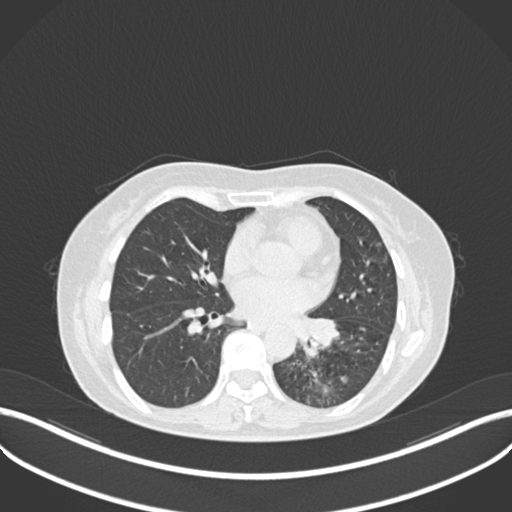
Chest CT, one axial slice; slice 119 of 270 in the series (ordered by position); 120 kVp; lung window (W 1500 / L -600 HU); 1 mm slice thickness; 512 × 512 image matrix, field of view 400 × 400 mm. Female patient, age 63 years. From the clinical record (not read from this slice): clinical TNM (as recorded): T1b N0 M0; histopathological grade: G2-3.
Outlined on this slice (rectangle marked by the reading radiologist):
- lung tumour (recorded histology: adenocarcinoma): box from (x=294, y=310) to (x=343, y=360) px